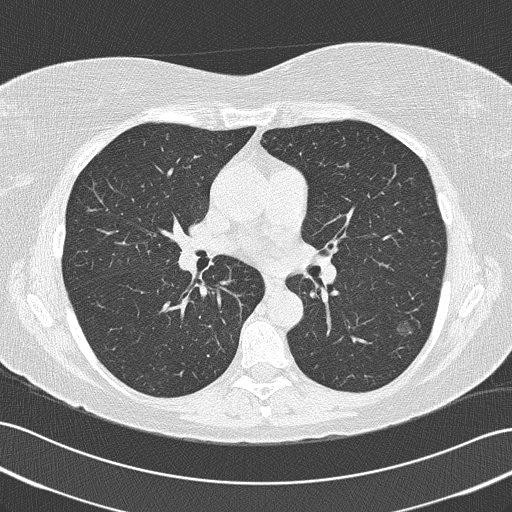
Low-dose screening chest CT, axial slice, baseline annual screen, lung window (W 1500 / L -600 HU), 2 mm slice thickness, slice 82 of 172 in the series, 512 × 512 image matrix. Female participant, aged 57 years at enrolment. Current smoker at enrolment.
Expert reader's lesion annotation, bounding box (x1, y1, x2, y2) in pixels: (383, 309, 429, 350). The exam's reader record, not a measurement of the box and not confirmed to be the same lesion: non-calcified nodule or mass ≥4 mm, left lower lobe, 11 × 11 mm, spiculated (stellate) margins, ground glass attenuation. Official screen result: positive, change unspecified: nodule(s) >= 4 mm or enlarging nodule(s), mass(es), or other non-specific abnormalities suspicious for lung cancer.